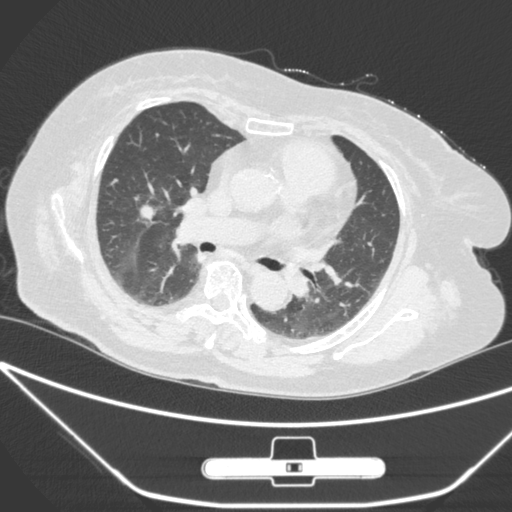
Chest CT, one axial slice; slice 153 of 245 in the series (ordered by position); 120 kVp; lung window (W 1500 / L -600 HU); 512 × 512 image matrix. Patient: female, 65 years. Case-level facts recorded for this patient, not image findings: clinical TNM (as recorded): T1c N0 M0.
Structures marked on this image (bounding box drawn by a radiologist):
- lung tumour (recorded histology: adenocarcinoma): box from (x=134, y=195) to (x=170, y=228) px